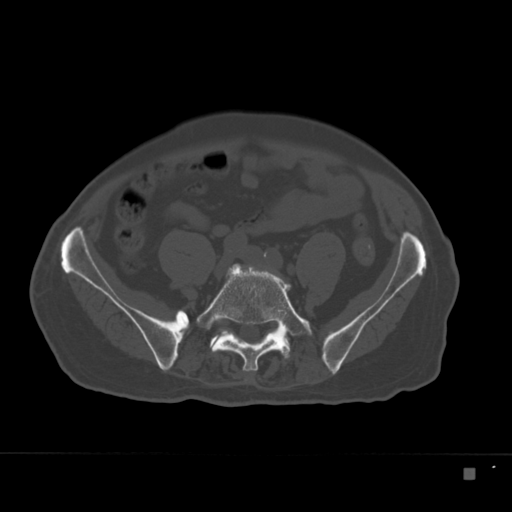
CT including the spine, one axial slice. Position 22 of 332 along the scan axis. Reconstruction kernel Br40s. 120 kVp. Bone window (W 1800 / L 400 HU). 1.5 mm slice thickness. 512 × 512 image matrix, field of view 389 × 389 mm. Patient: male, 72 years. Case-level facts recorded for this patient, not image findings: primary cancer: skeletal.
Structures marked on this image (semi-automatic segmentation, software-assisted and operator-edited):
- L5 vertebra: bounding box (x1, y1, x2, y2) in pixels: (196, 264, 312, 372)